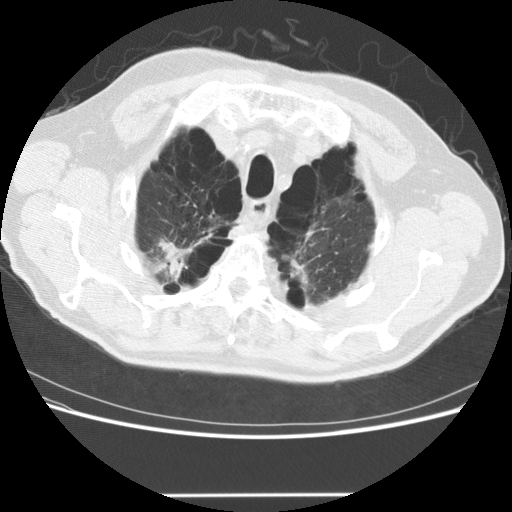
Low-dose screening chest CT, one axial slice. Position 123 of 151 along the scan axis. Reconstruction kernel STANDARD. Lung window (W 1500 / L -600 HU). 512 × 512 image matrix, field of view 360 × 360 mm.
Annotated regions visible in this slice (manually delineated by an expert):
- lesion 1 (tumor, upper lobe of right lung): bounding box <160,241,192,280> (left, top, right, bottom; pixels)